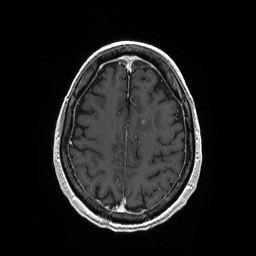
Brain MRI from a brain-tumour surgery series, one axial slice. Slice 67 of 208 in the series (ordered by position). T1-weighted post-contrast. 256 × 256 image matrix, field of view 256 × 256 mm. Case-level facts recorded for this patient, not image findings: histopathology: Primary diffuse large B-cell lymphoma; tumour location: Left Corpus Callosum (Frontal).
Structures marked on this image (outlined manually by an expert reader):
- tumour: bounding box [x1, y1, x2, y2] px = [142, 120, 146, 125]